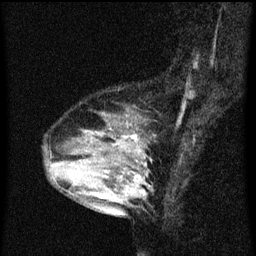
Breast MRI (dynamic contrast-enhanced), one sagittal slice; dynamic contrast-enhanced series, image 2 of 3 at this slice position (ordered by acquisition); 1.5 T; TE 4.2 ms, TR 8 ms; 2 mm slice thickness; 256 × 256 image matrix, field of view 180 × 180 mm. Patient: female, 33 years.
Structures marked on this image (semi-automatically segmented with operator editing):
- analysis volume of interest (the breast-tissue region the enhancement analysis was run in; not a lesion): bounding box (x1, y1, x2, y2) in pixels: (61, 126, 147, 213)
- tumour enhancement mask (voxels above the 70 % enhancement threshold inside the analysis volume of interest): (125, 136, 144, 197)